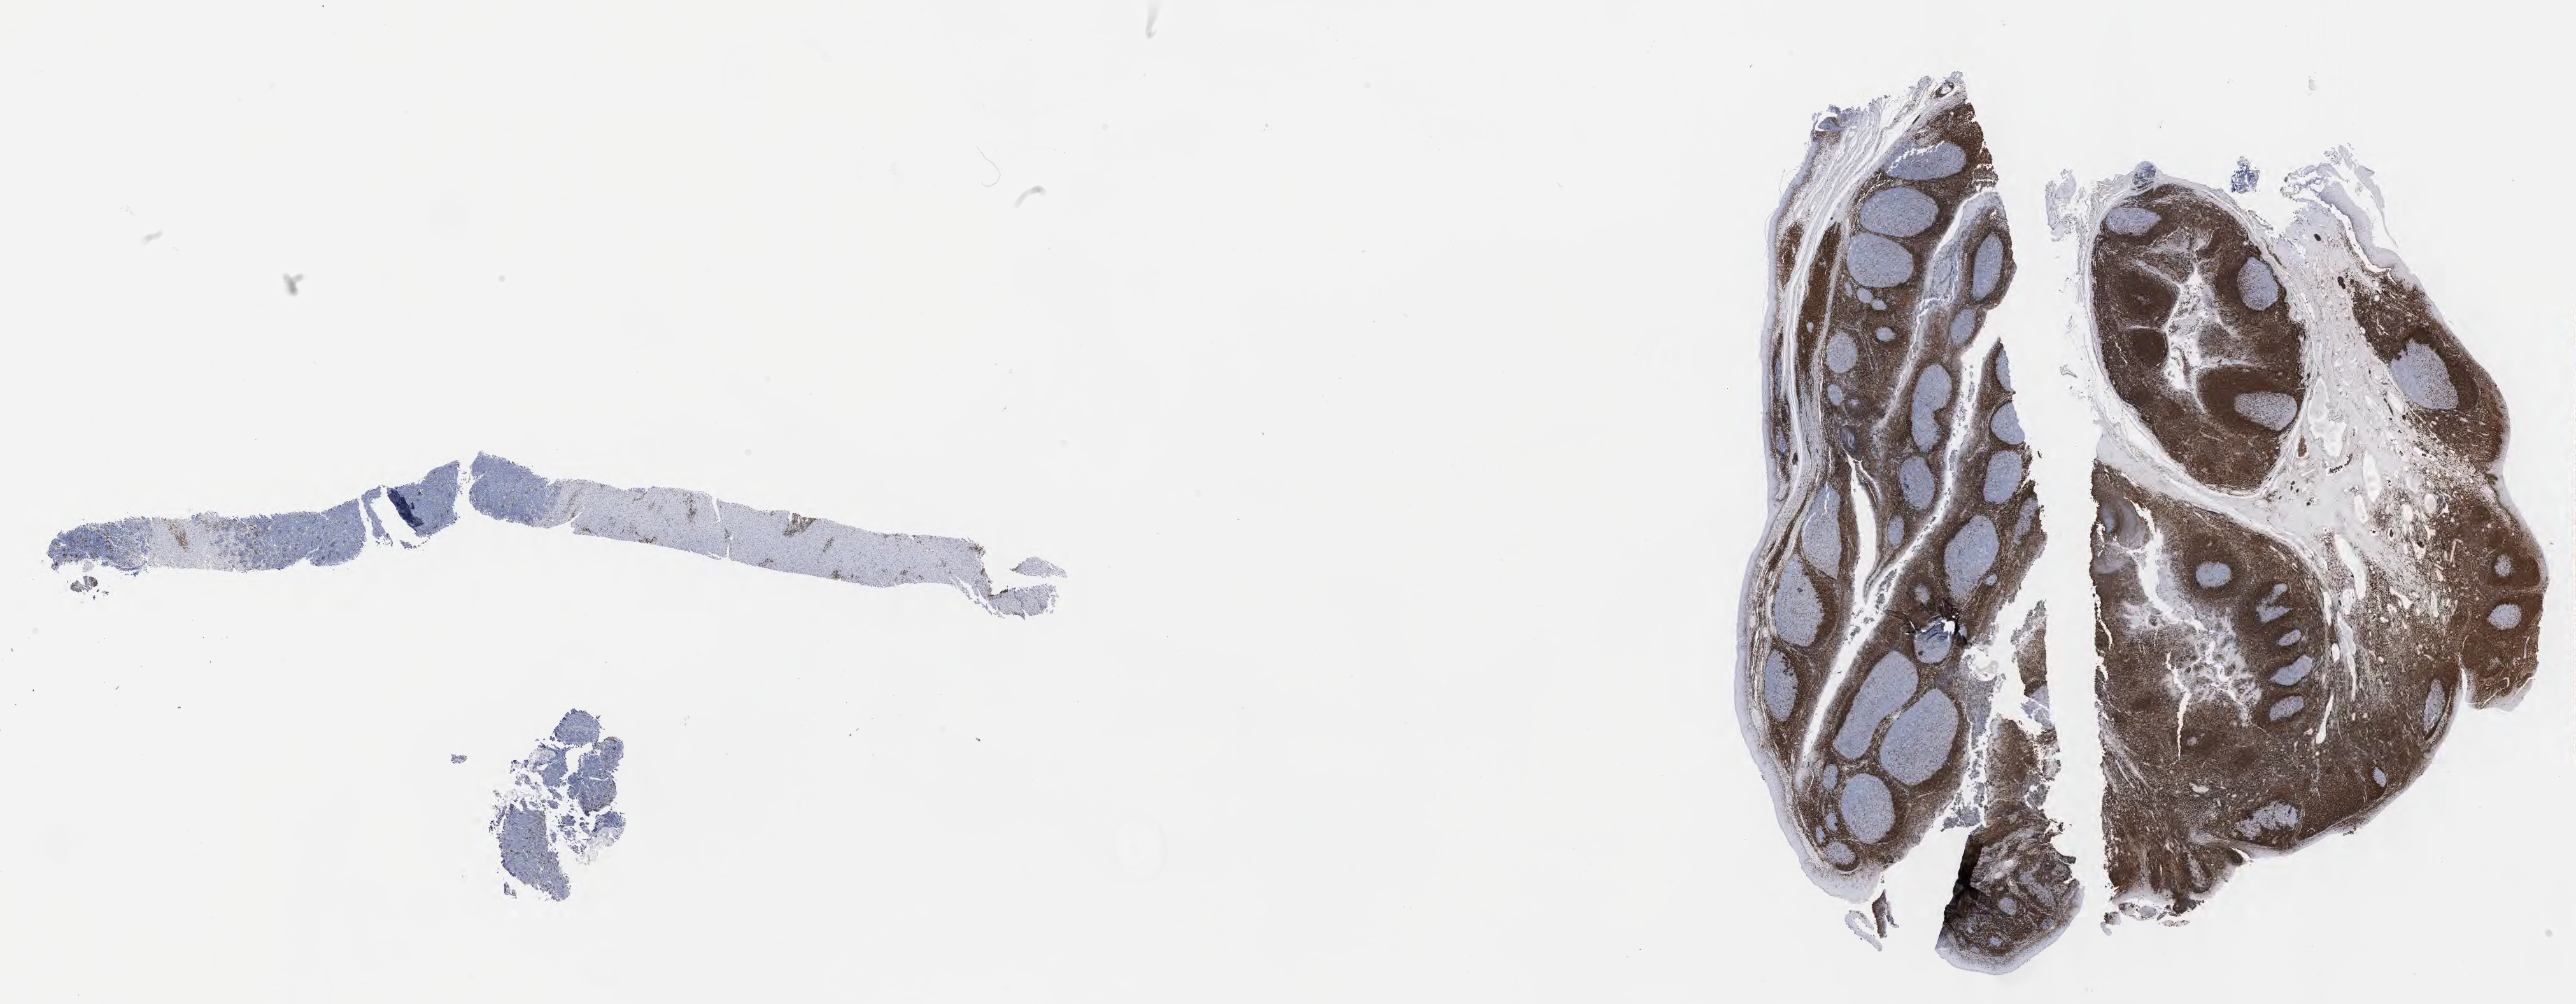
Whole-slide image, immunohistochemical stain for BCL2 — low-resolution overview of the scanned area, about 32.7 x 12.7 mm. Tumor tissue. Patient male; age 68 years.
Histologic diagnosis: Burkitt lymphoma, NOS.